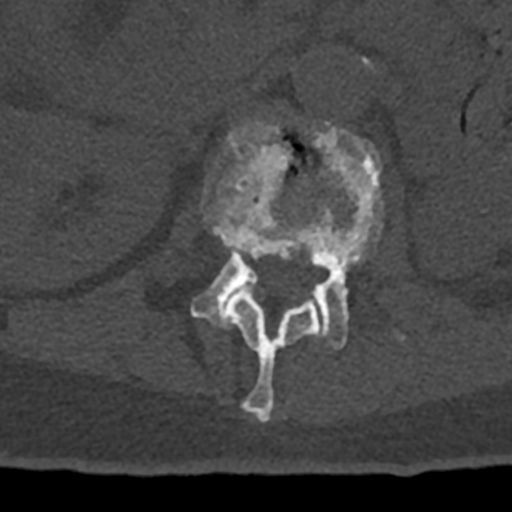
CT including the spine, one axial slice; slice 406 of 797 in the series (ordered by position); reconstruction kernel Br40s/3; 120 kVp; bone window (W 1800 / L 400 HU); 0.5 mm slice thickness; 512 × 512 image matrix, field of view 160 × 160 mm. Male patient, age 74 years. From the clinical record (not read from this slice): primary cancer: renal; vertebrae with lytic lesions (as recorded): T10, L1, L2, L3, L4, L5.
Structures marked on this image (semi-automatically segmented with operator editing):
- L1 vertebra: box from (x=201, y=120) to (x=319, y=422) px
- L2 vertebra: (x=191, y=123)–(x=404, y=350)